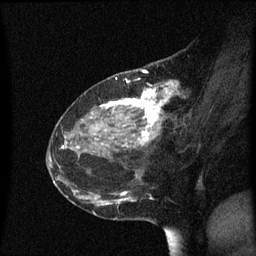
Breast MRI (dynamic contrast-enhanced), one sagittal slice; position 26 of 60 along the scan axis; dynamic contrast-enhanced series, image 2 of 3 at this slice position (ordered by acquisition); 1.5 T; TE 4.2 ms, TR 8.4 ms; 2 mm slice thickness; 256 × 256 image matrix, field of view 200 × 200 mm. Female patient, age 48 years. From the clinical record (not read from this slice): setting: breast cancer imaged before/during neoadjuvant chemotherapy; receptor status: HR-positive, HER2-negative.
Annotated regions visible in this slice (semi-automatic segmentation, software-assisted and operator-edited):
- analysis volume of interest (the breast-tissue region the enhancement analysis was run in; not a lesion): bounding box <80,78,191,221> (left, top, right, bottom; pixels)
- tumour enhancement mask (voxels above the 70 % enhancement threshold inside the analysis volume of interest): <92,83,177,202>